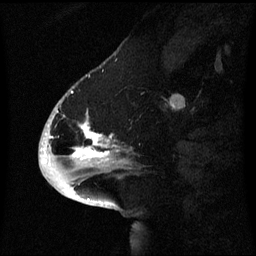
Breast MRI (dynamic contrast-enhanced), one sagittal slice. Position 22 of 60 along the scan axis. Dynamic contrast-enhanced series, image 2 of 3 at this slice position (ordered by acquisition). 1.5 T. TE 4.2 ms, TR 8.4 ms. 2.1 mm slice thickness. 256 × 256 image matrix, field of view 220 × 220 mm. Patient: female, 53 years. Case-level facts recorded for this patient, not image findings: setting: breast cancer imaged before/during neoadjuvant chemotherapy; receptor status: HR-positive, HER2-negative.
Annotated regions visible in this slice (semi-automatically segmented with operator editing):
- analysis volume of interest (the breast-tissue region the enhancement analysis was run in; not a lesion): bounding box (x1, y1, x2, y2) in pixels: (52, 90, 131, 171)
- tumour enhancement mask (voxels above the 70 % enhancement threshold inside the analysis volume of interest): (56, 108, 111, 161)